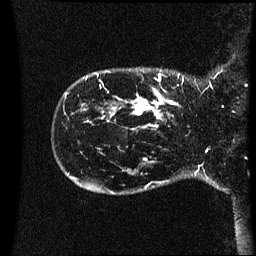
Breast MRI (dynamic contrast-enhanced), one sagittal slice. Position 7 of 60 along the scan axis. Dynamic contrast-enhanced series, image 2 of 3 at this slice position (ordered by acquisition). 1.5 T. TE 4.2 ms, TR 8.4 ms. 2.2 mm slice thickness. 256 × 256 image matrix. Patient: female, 41 years. Case-level facts recorded for this patient, not image findings: setting: breast cancer imaged before/during neoadjuvant chemotherapy; receptor status: HER2-positive.
Outlined on this slice (semi-automatic segmentation, software-assisted and operator-edited):
- analysis volume of interest (the breast-tissue region the enhancement analysis was run in; not a lesion): bounding box [x1, y1, x2, y2] px = [122, 80, 197, 121]
- tumour enhancement mask (voxels above the 70 % enhancement threshold inside the analysis volume of interest): [134, 90, 180, 119]